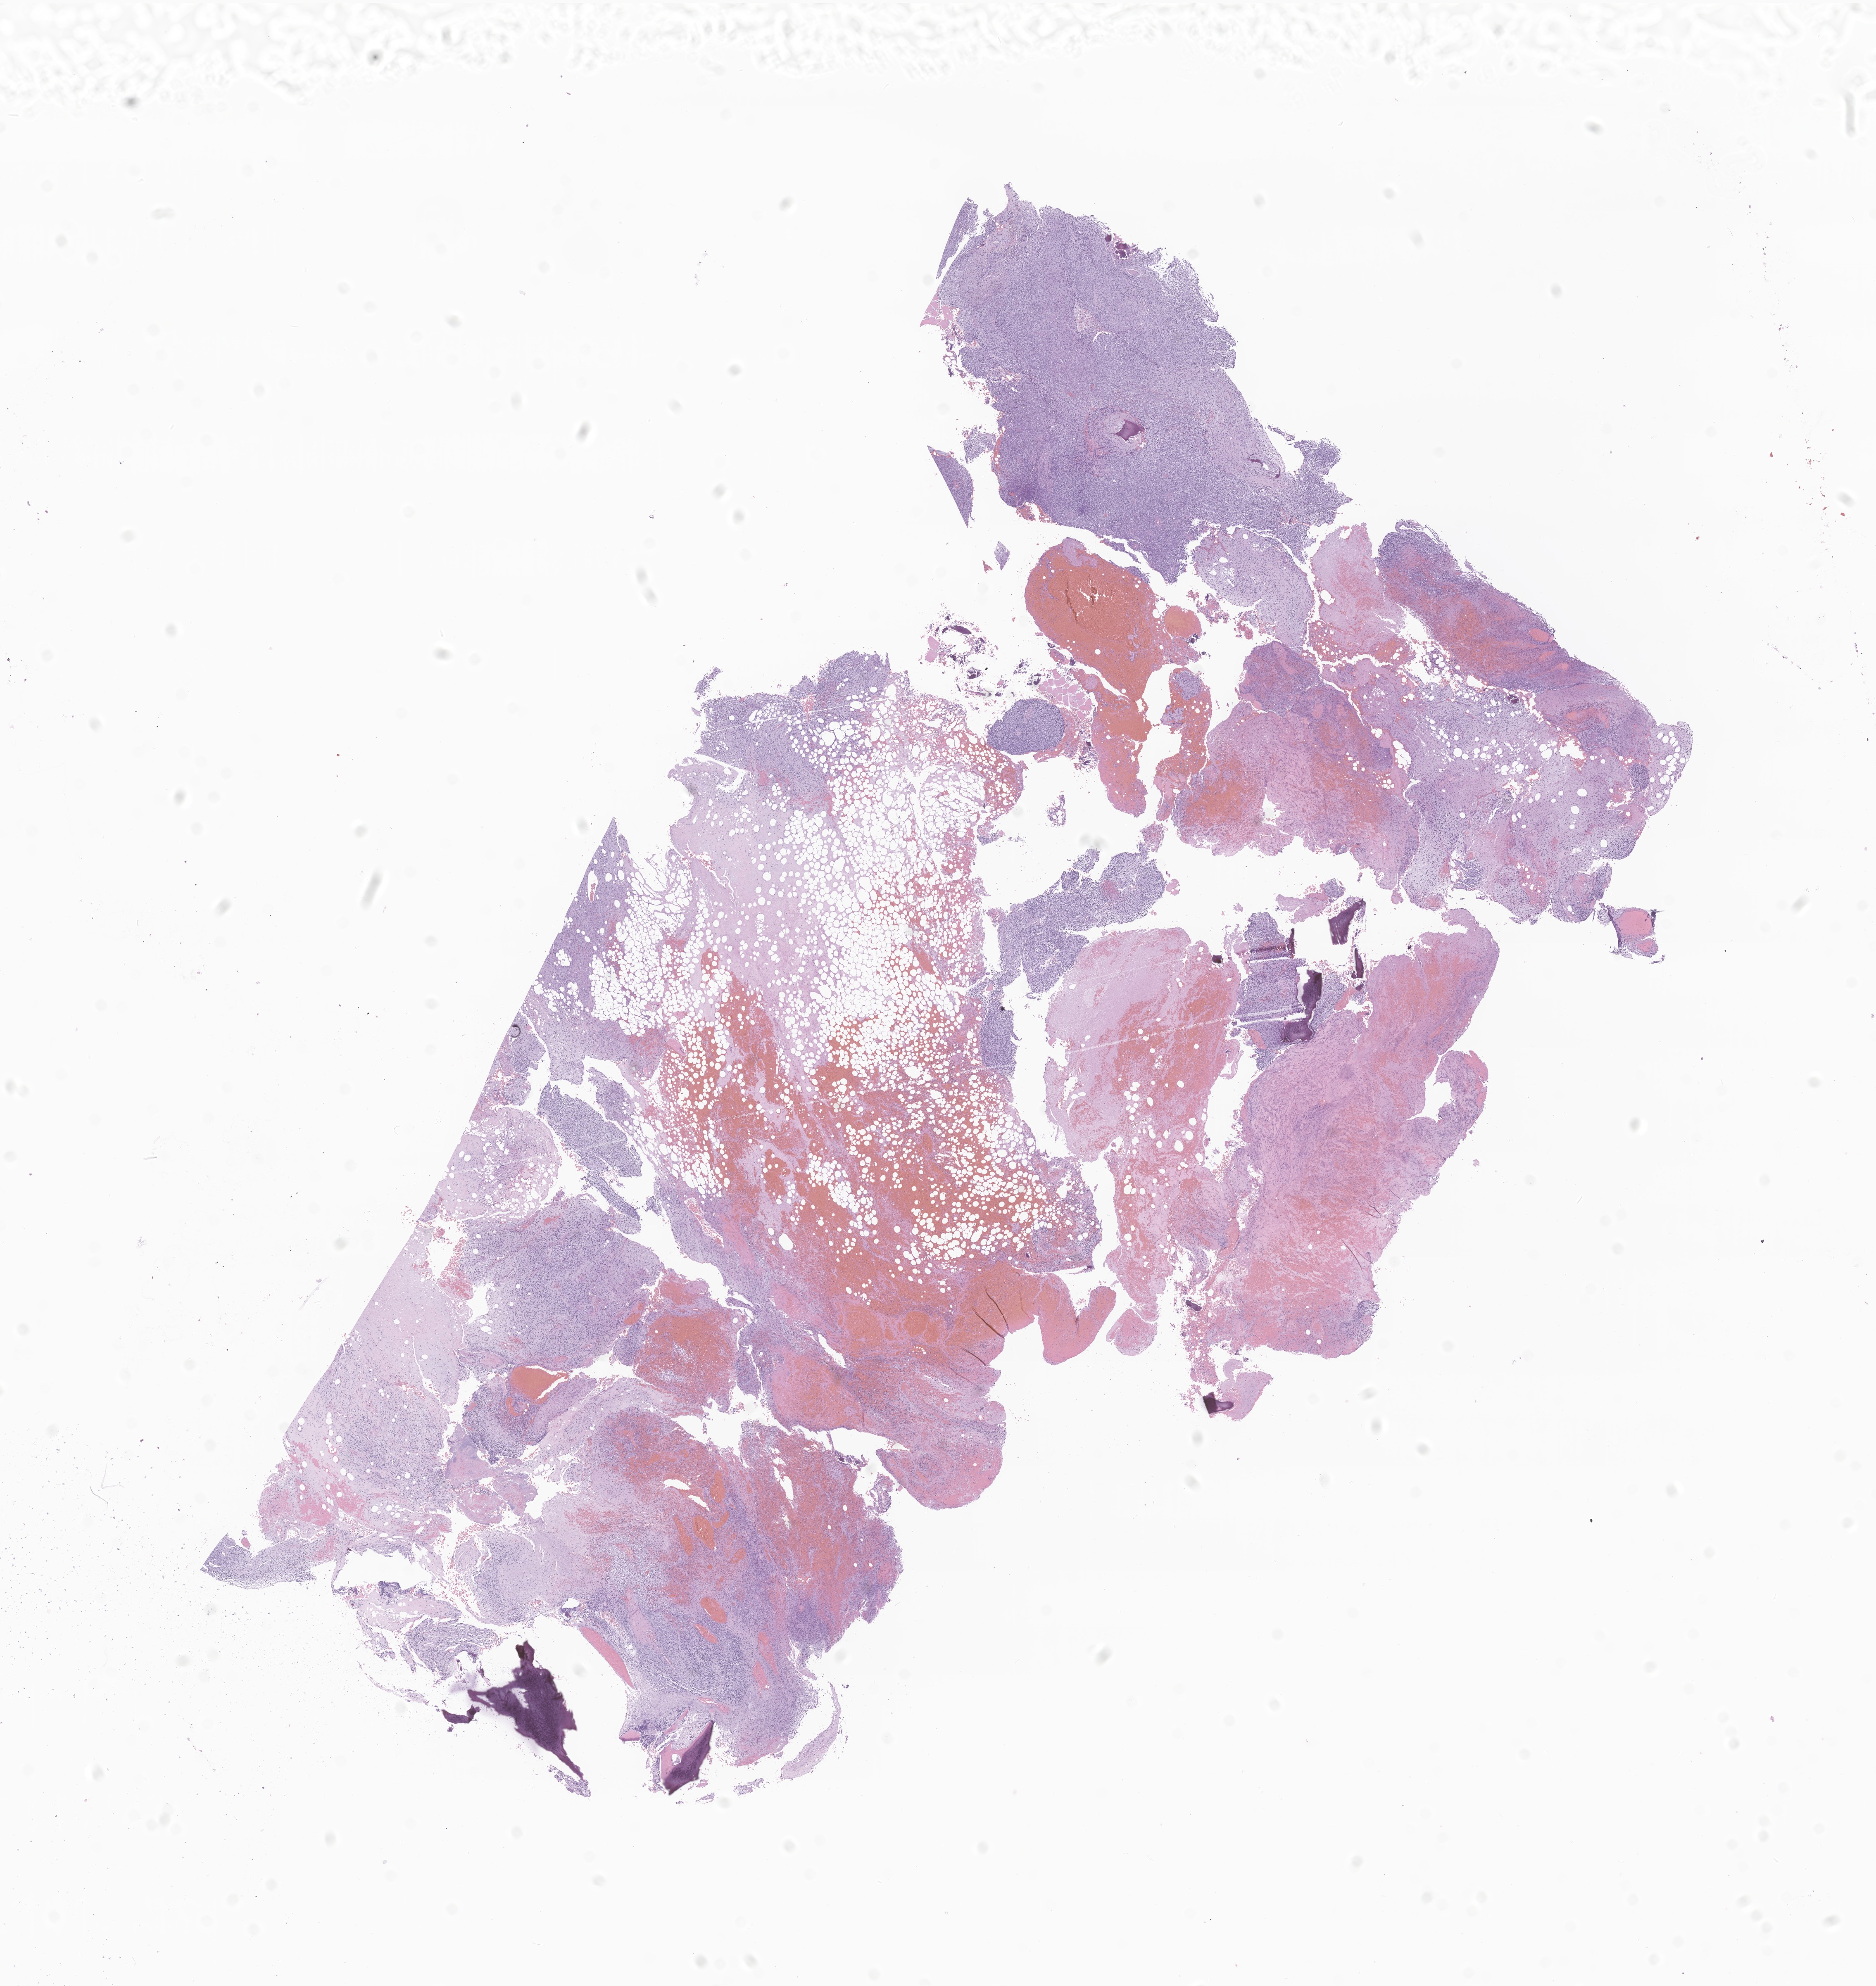
Digitized hematoxylin and eosin (H&E)-stained section of tumor tissue from the long bone of lower limb — low-resolution overview of the scanned area, about 19.1 x 20.3 mm. Formalin-fixed, paraffin-embedded (FFPE) tissue. Patient: male, age 315 months (26 years 3 months).
- recorded diagnosis: Embryonal rhabdomyosarcoma, NOS